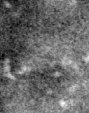
Cropped region of a digitized screen-film mammogram centred on a radiologist-marked abnormality; right breast; CC view.
Calcifications, morphology pleomorphic, distribution clustered; BI-RADS assessment category 4; pathology (as recorded): malignant.